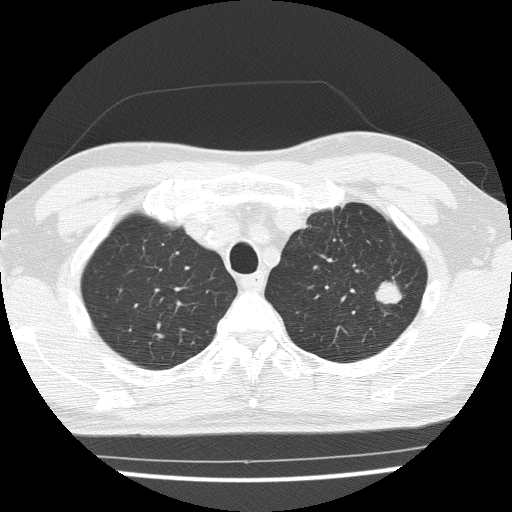
Low-dose screening chest CT, one axial slice. Slice 122 of 154 in the series (ordered by position). Lung window (W 1500 / L -600 HU). 512 × 512 image matrix.
Structures marked on this image (outlined manually by an expert reader):
- lesion 1 (tumor, upper lobe of left lung): bounding box <376,277,402,304> (left, top, right, bottom; pixels)